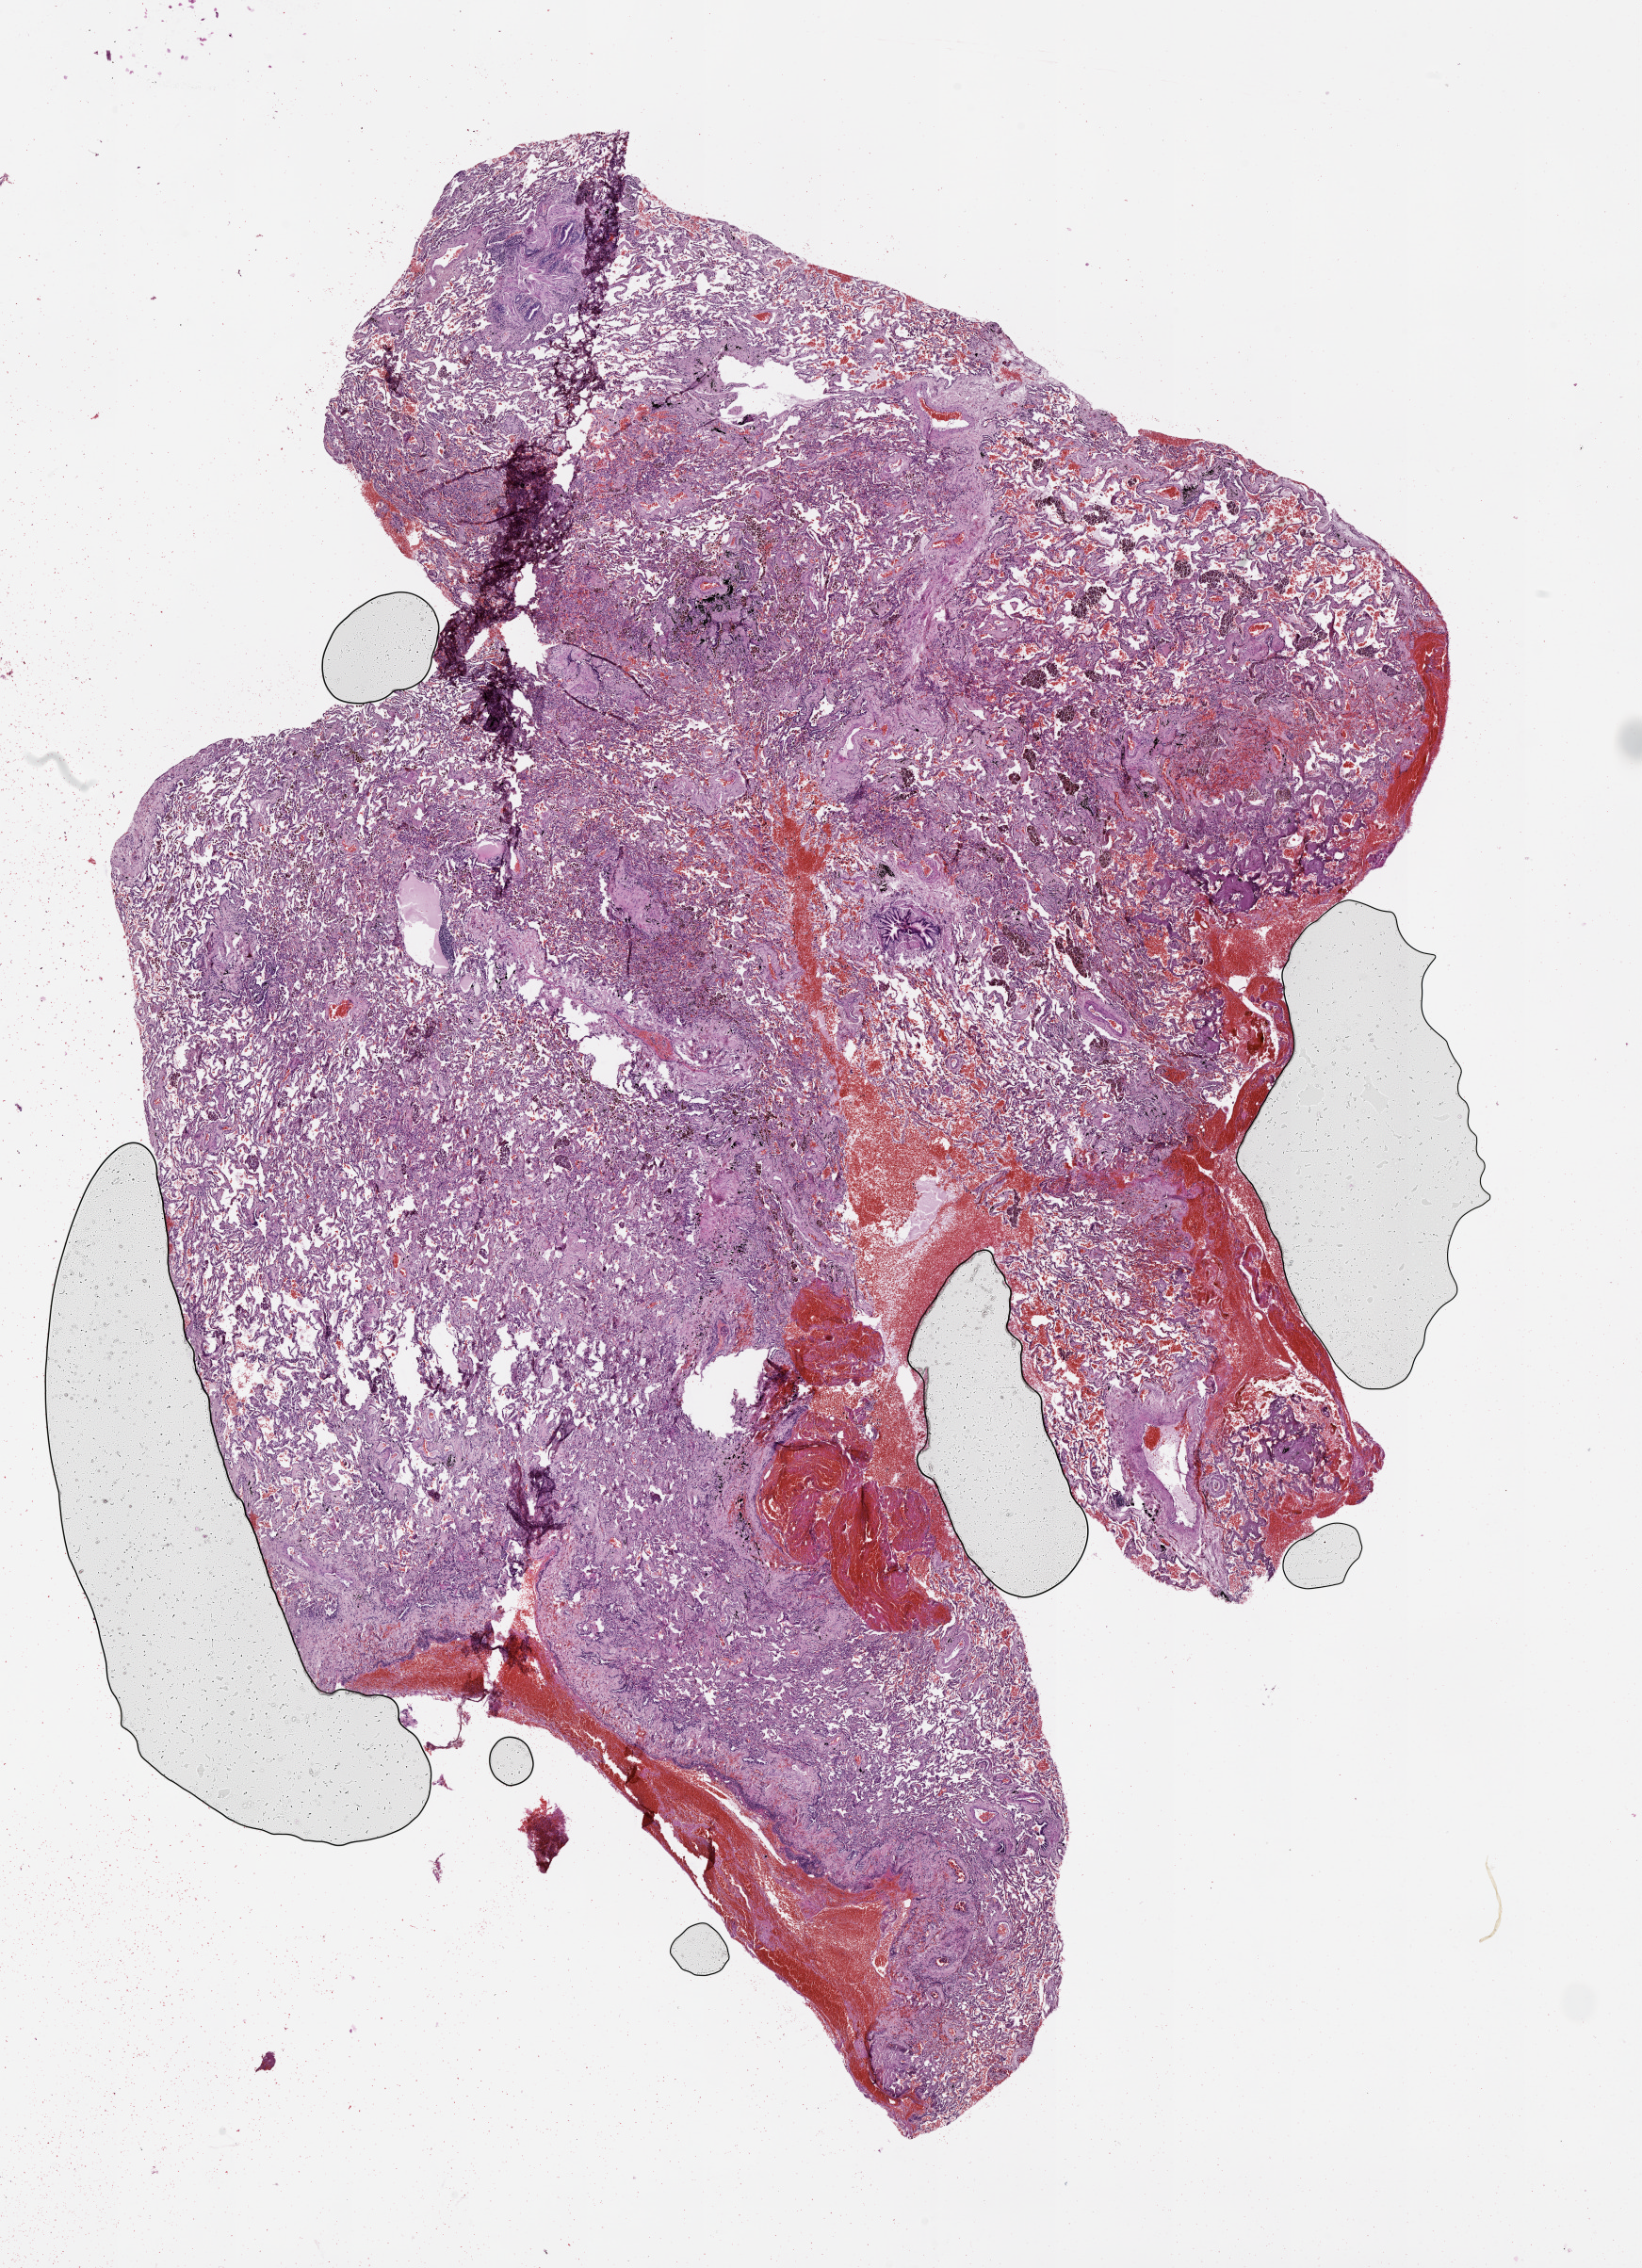
Digitized H&E tissue section (whole slide) — shown as a low-resolution overview of the whole scanned area (about 14.0 x 19.4 mm); normal (non-tumour) tissue sample, lung. Female, 56 y/o.
This section: normal (non-tumour) tissue from the same patient. Patient diagnosis (cohort enrolment): squamous cell carcinoma (lung).